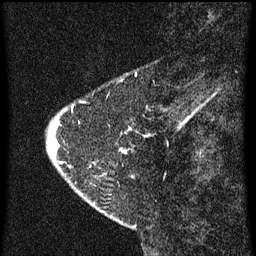
Breast MRI (dynamic contrast-enhanced), one sagittal slice; position 14 of 60 along the scan axis; dynamic contrast-enhanced series, image 2 of 3 at this slice position (ordered by acquisition); 1.5 T; TE 4.2 ms, TR 8 ms; 2 mm slice thickness; 256 × 256 image matrix. Patient: female, 47 years.
Structures marked on this image (semi-automatically segmented with operator editing):
- analysis volume of interest (the breast-tissue region the enhancement analysis was run in; not a lesion): box from (x=46, y=104) to (x=149, y=199) px
- tumour enhancement mask (voxels above the 70 % enhancement threshold inside the analysis volume of interest): (x=60, y=128)–(x=131, y=165)